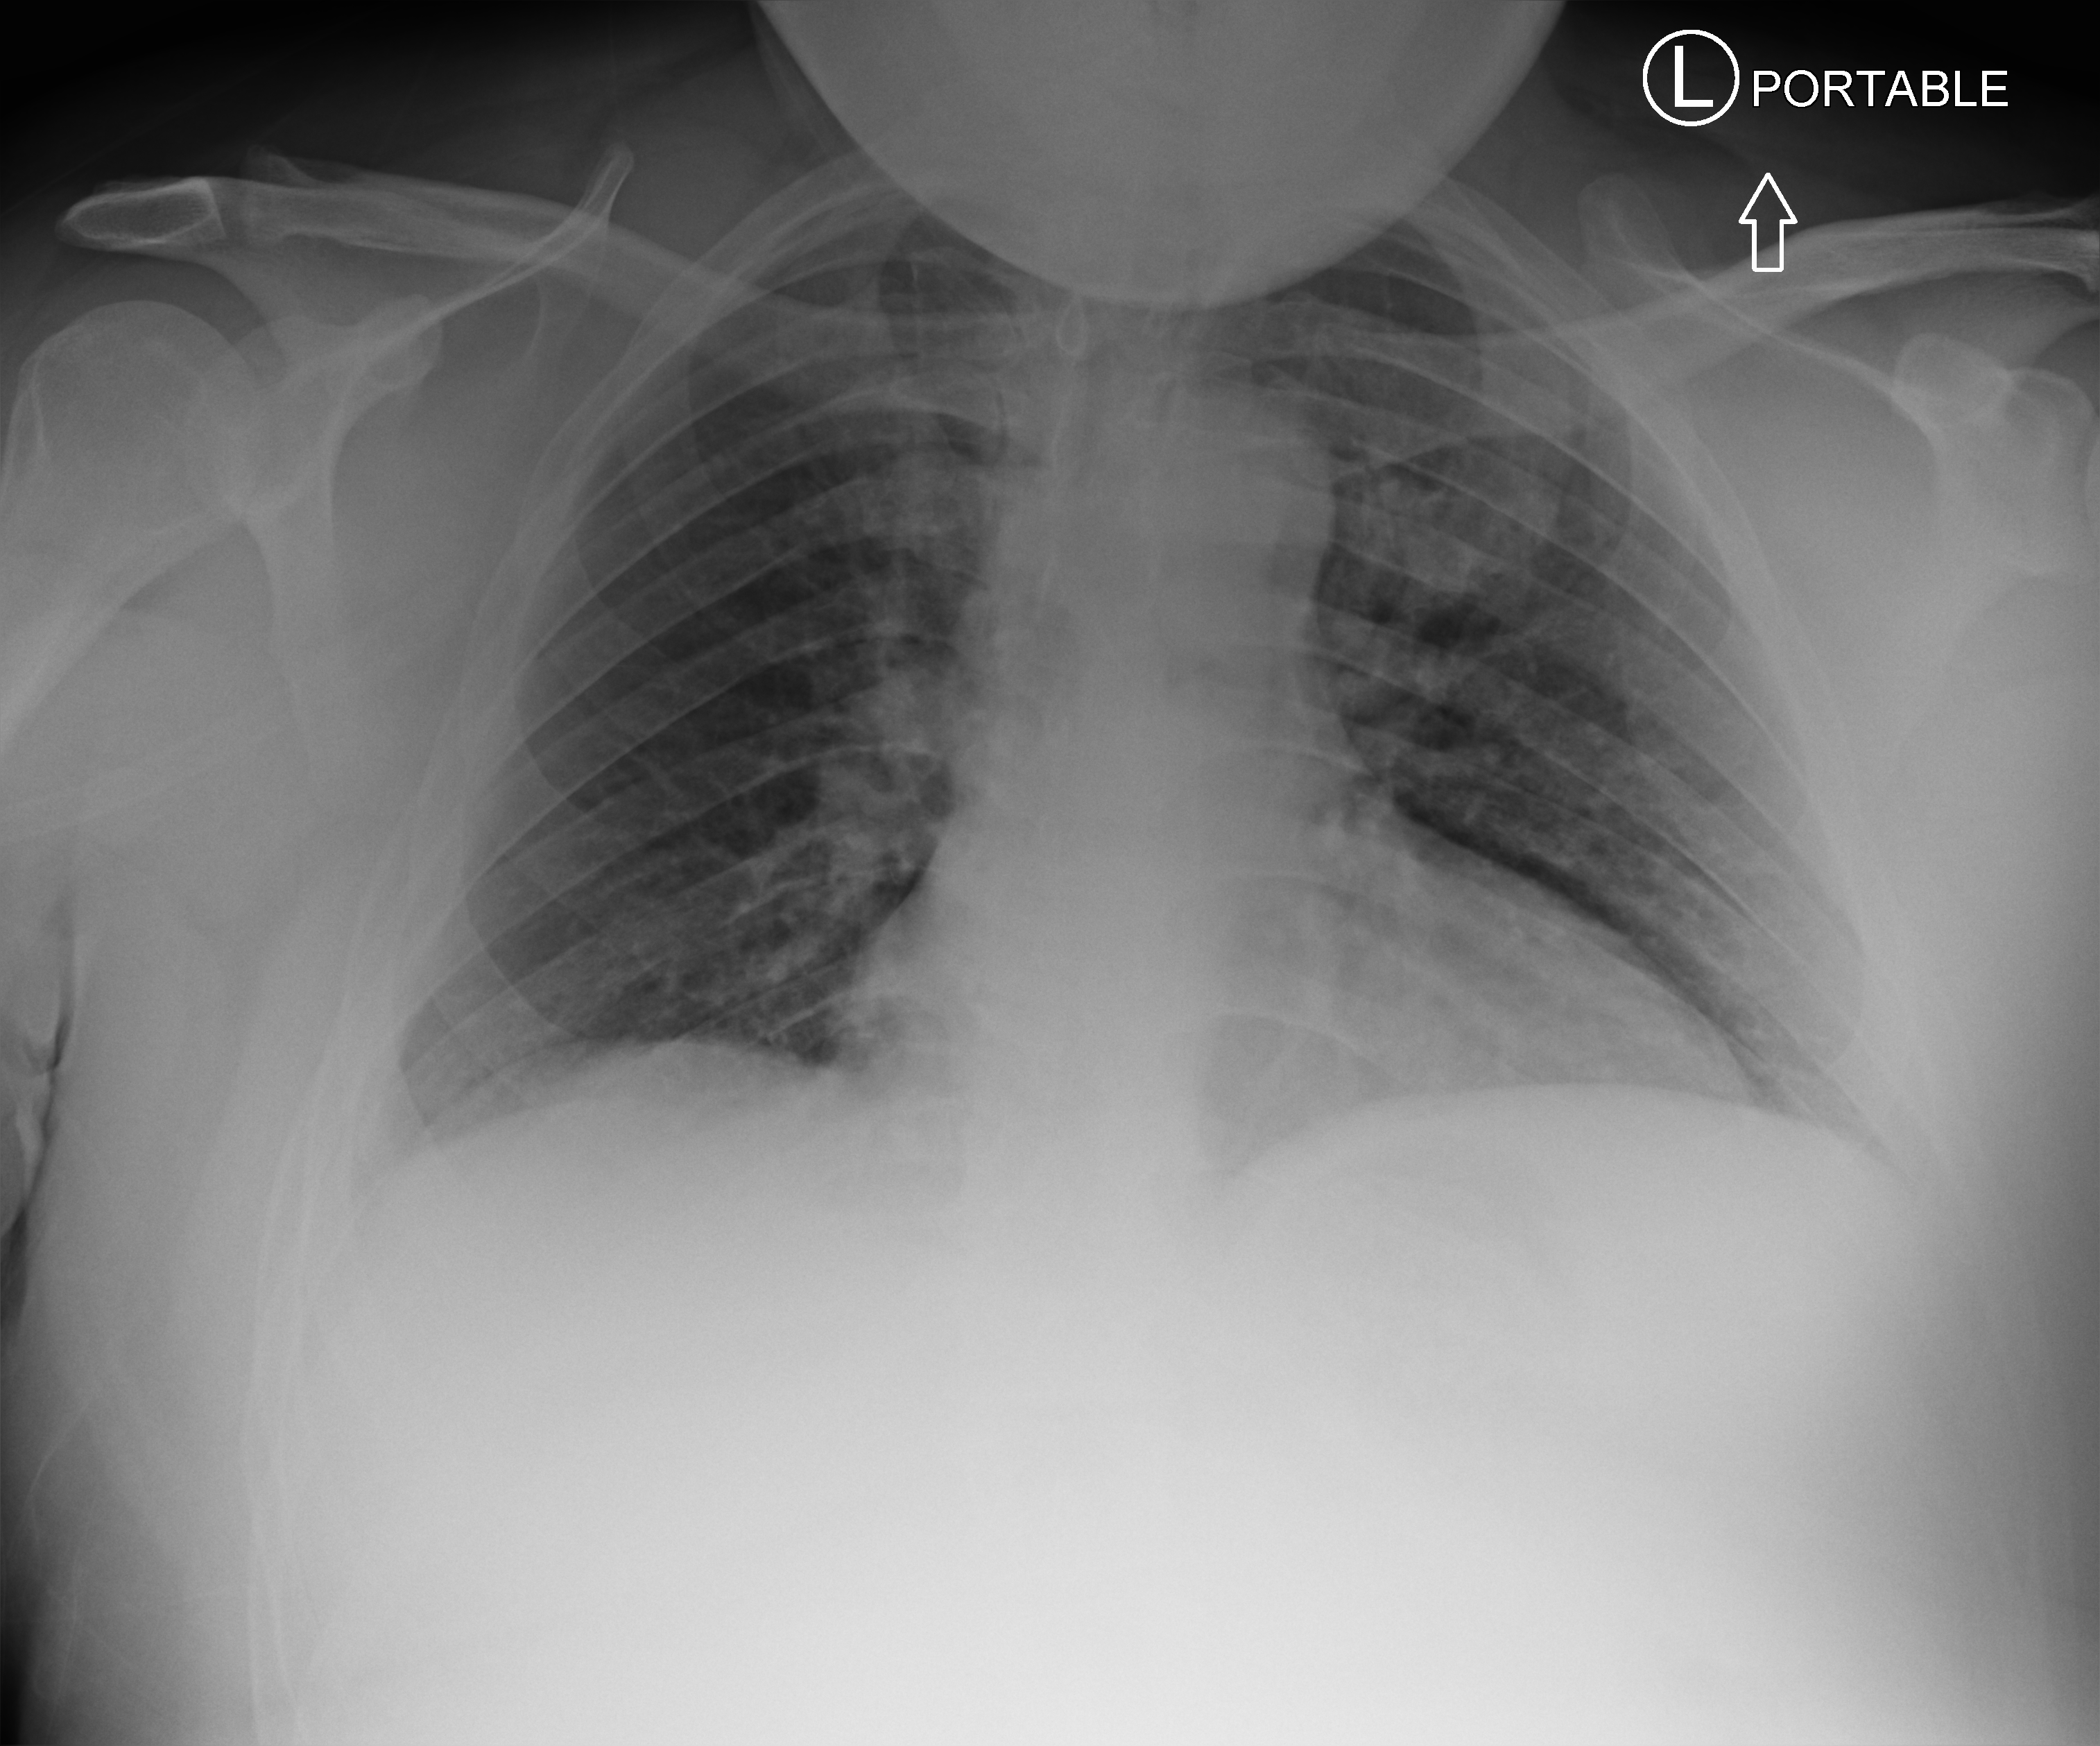
Bedside chest radiograph (computed radiography). Male patient hospitalised with COVID-19, age 18–59 years.
From the hospital-stay record, not from the radiograph (when in the stay this image was taken is not recorded): chronic kidney disease (admission record): no; COPD (admission record): no.